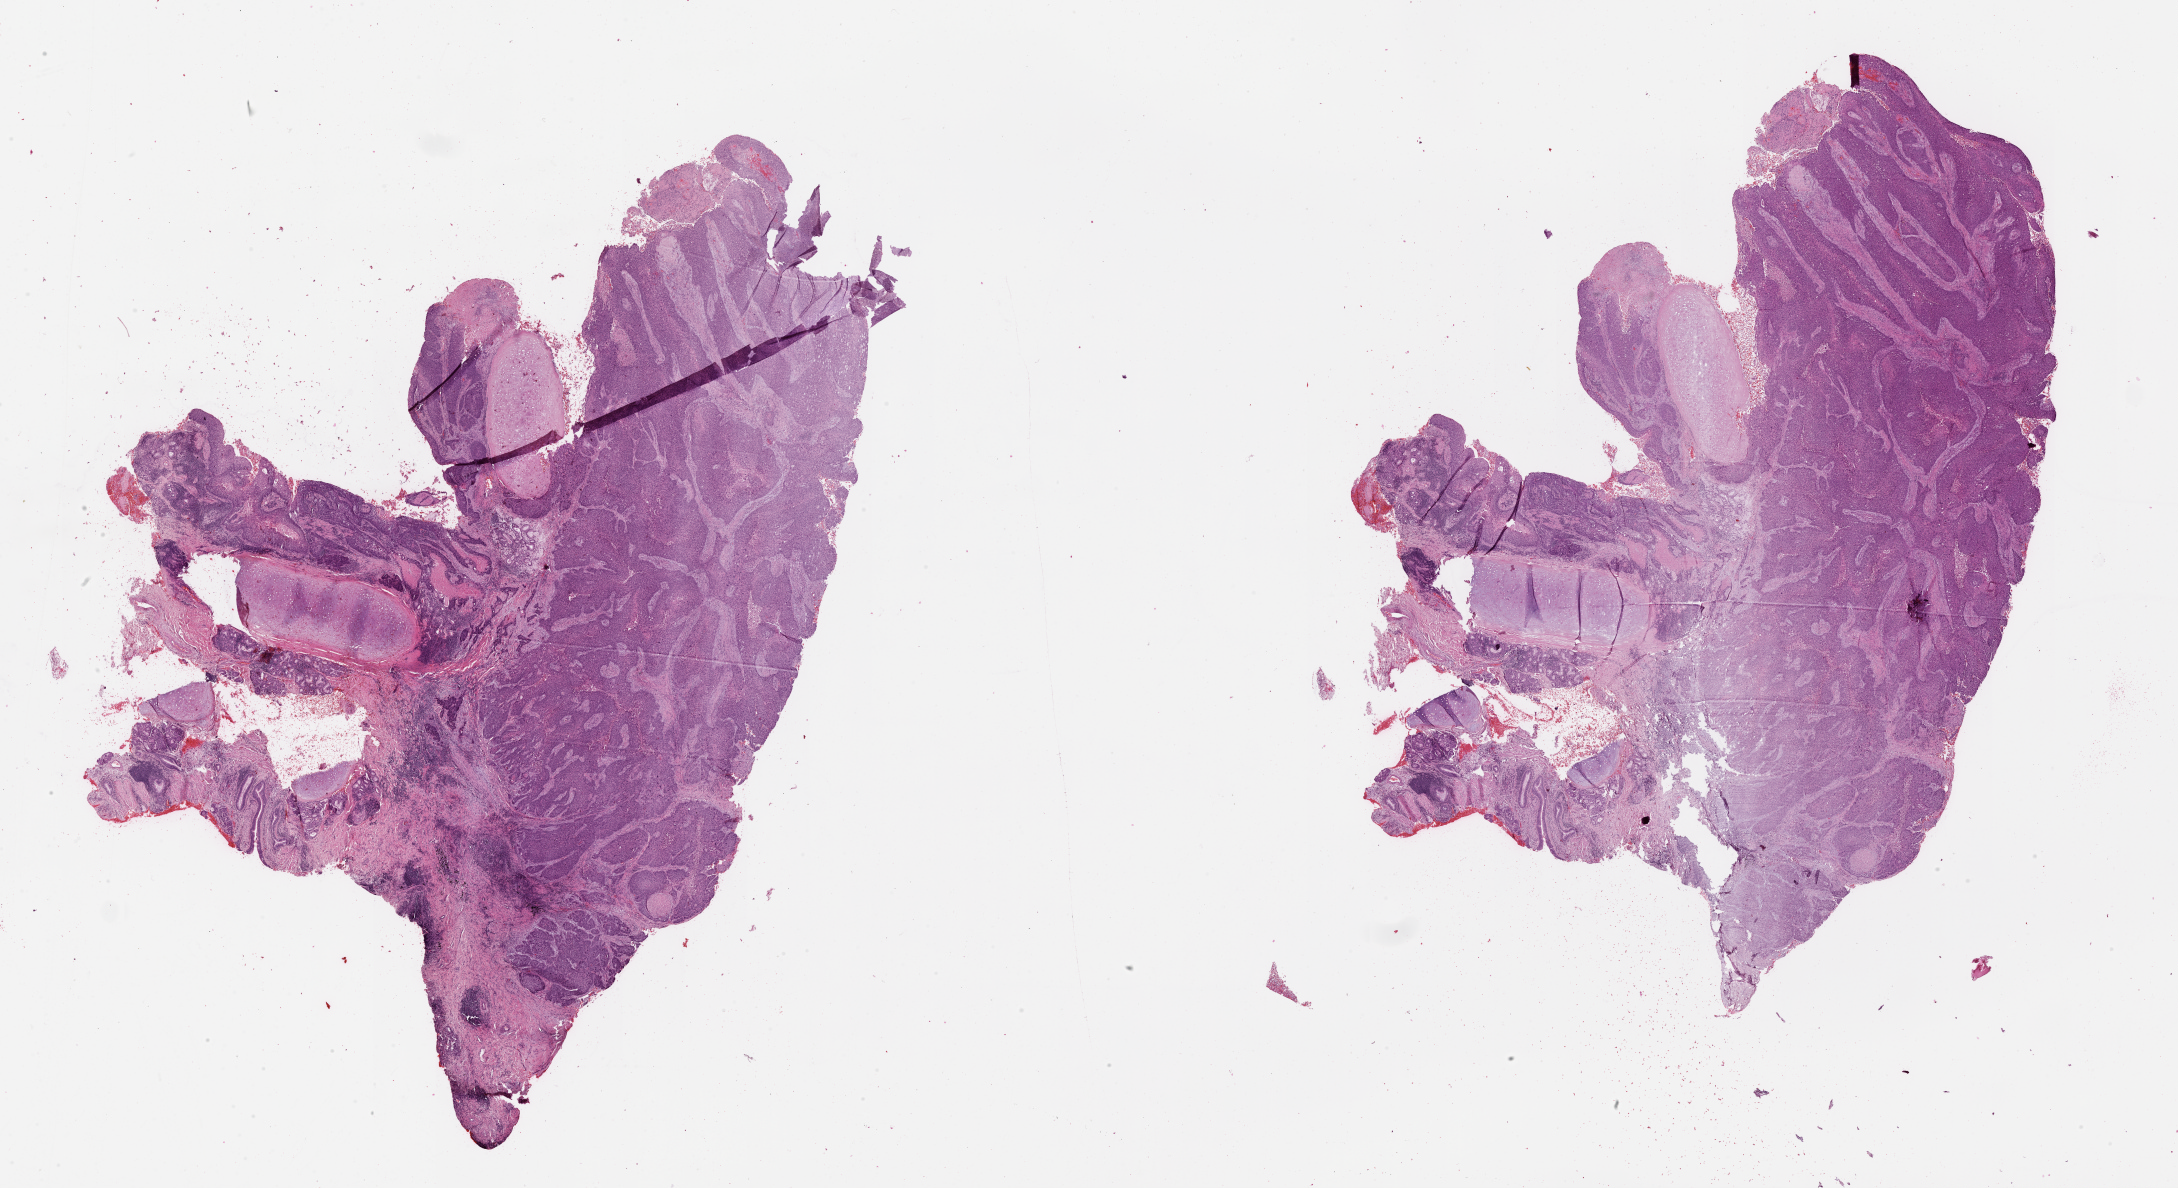
Digitized H&E-stained tissue section (whole slide) — whole scanned area (about 35.1 x 19.1 mm, acquisition: 20x scan) shown as a low-resolution overview. Lung, tumour tissue. Patient: male, age 43 years.
Patient diagnosis (cohort enrolment): squamous cell carcinoma (lung).